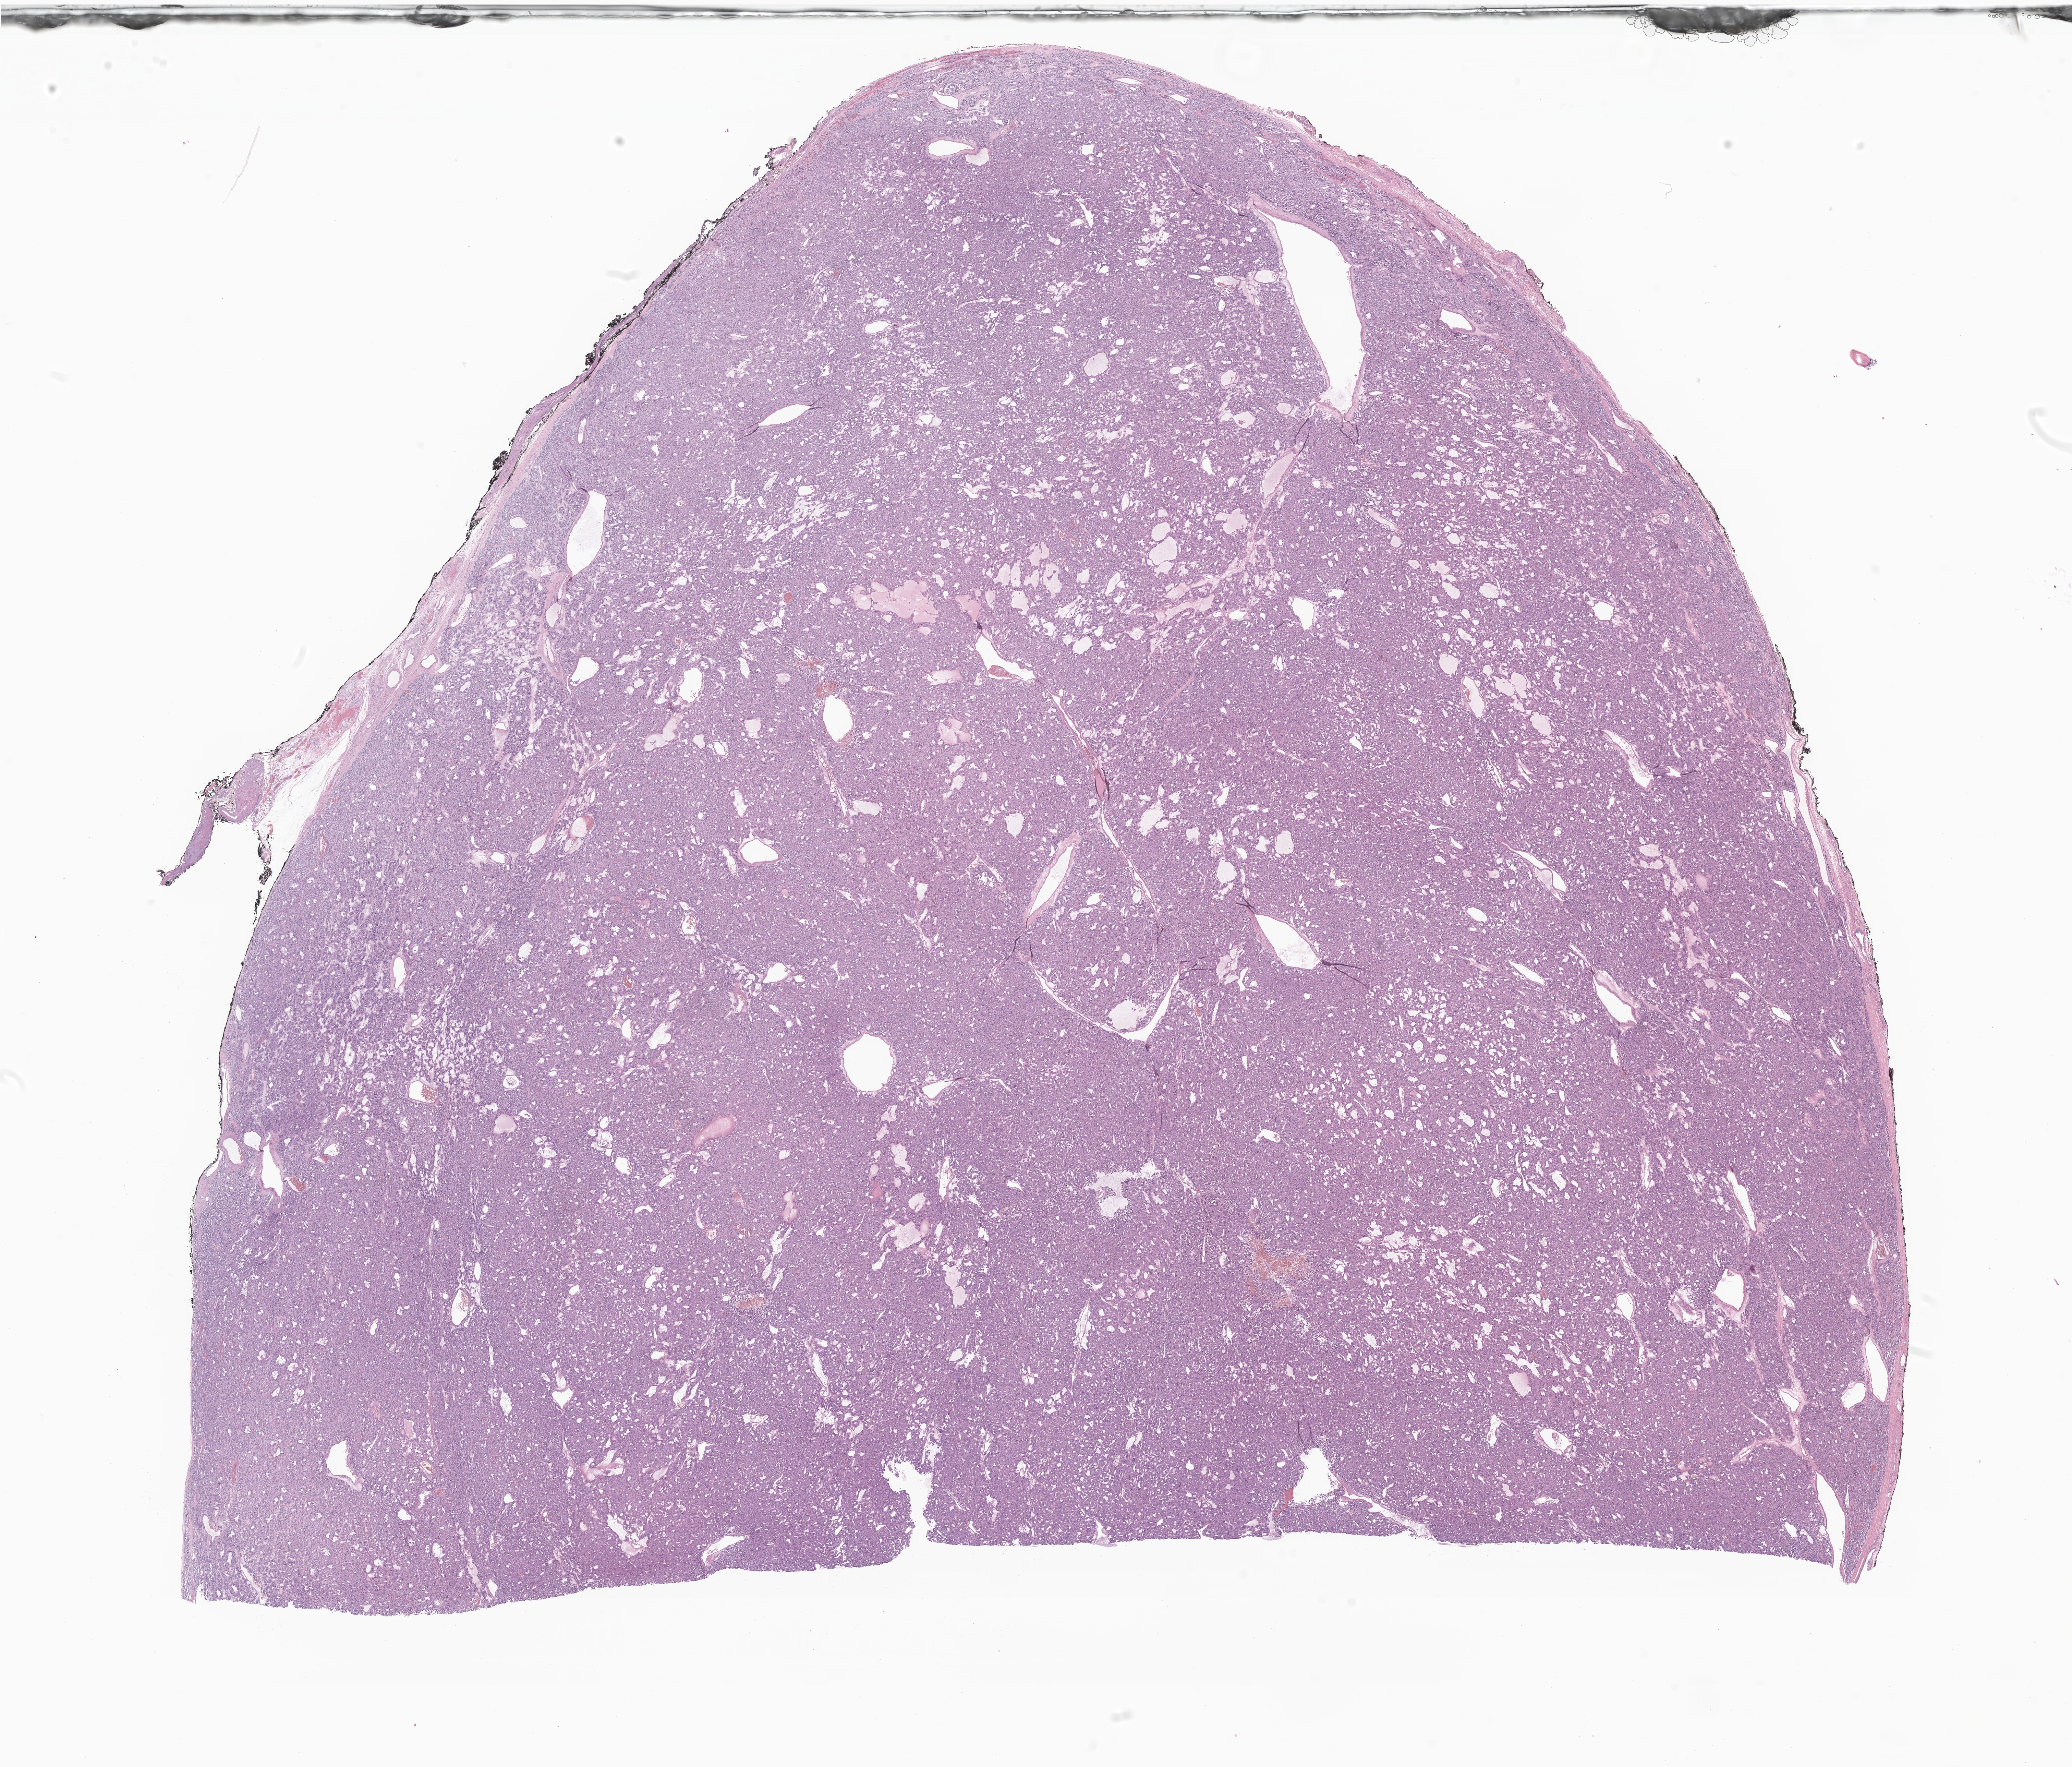
Digitized hematoxylin and eosin (H&E)-stained section of tumor tissue from the retroperitoneum — a low-resolution overview of the entire scanned area, about 25.5 x 21.7 mm. Patient male; age 160 months (13 years 4 months).
- specimen: formalin-fixed paraffin-embedded section